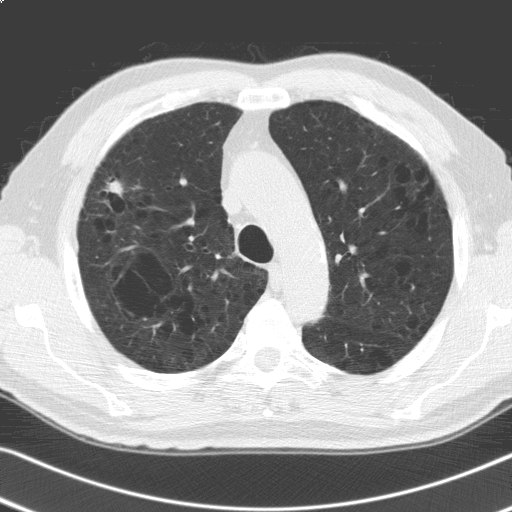
Low-dose screening chest CT, axial slice, second screening round (one year after baseline), lung window (W 1500 / L -600 HU), standard (soft-tissue) reconstruction kernel (C), slice 42 of 168 in the series. Male participant, aged 69 years at enrolment.
Expert reader's lesion annotation, box from (x=85, y=167) to (x=132, y=213) px. The screening reader recorded 6 non-calcified nodules or masses ≥4 mm on this exam; which of them this box marks is not recorded. Participant outcome: lung cancer diagnosed 91 days after this screen — adenosquamous carcinoma, right upper lobe, poorly differentiated (G3), stage IV (AJCC 6th edition), 30 mm at pathology.